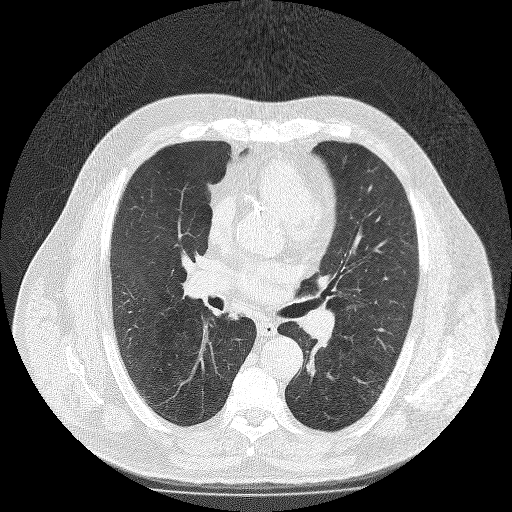
Chest CT (low-dose screening protocol), one axial image; second screening round (one year after baseline); lung window (W 1500 / L -600 HU); 2 mm slice thickness; slice 82 of 188 in the series; 512 × 512 image matrix, field of view 420 × 420 mm. Male participant, aged 65 years at enrolment. Former smoker at enrolment.
Expert-annotated lung lesion, bounding box (x1, y1, x2, y2) in pixels: (210, 301, 253, 332). The exam's reader record, not a measurement of the box and not confirmed to be the same lesion: non-calcified nodule or mass ≥4 mm, right lower lobe, 10 × 9 mm, spiculated (stellate) margins, soft tissue attenuation, pre-existing on the prior screen: yes; interval growth: no.